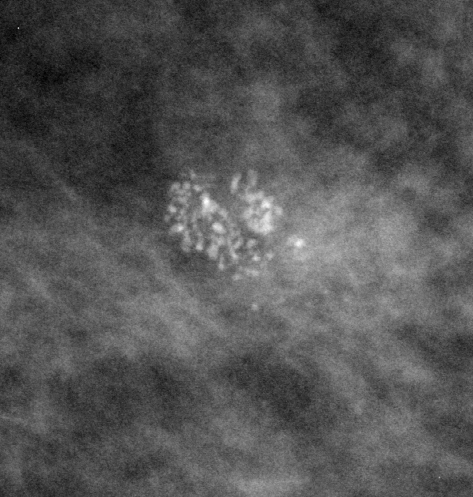
Region of interest cut from a scanned film mammogram (one marked finding); left breast; MLO view; BI-RADS breast density category 2 (scale 1–4).
Finding: calcifications, morphology pleomorphic, distribution clustered; BI-RADS assessment category 4; subtlety rating 5 on a 1 (subtle) to 5 (obvious) scale; pathology (as recorded): malignant.